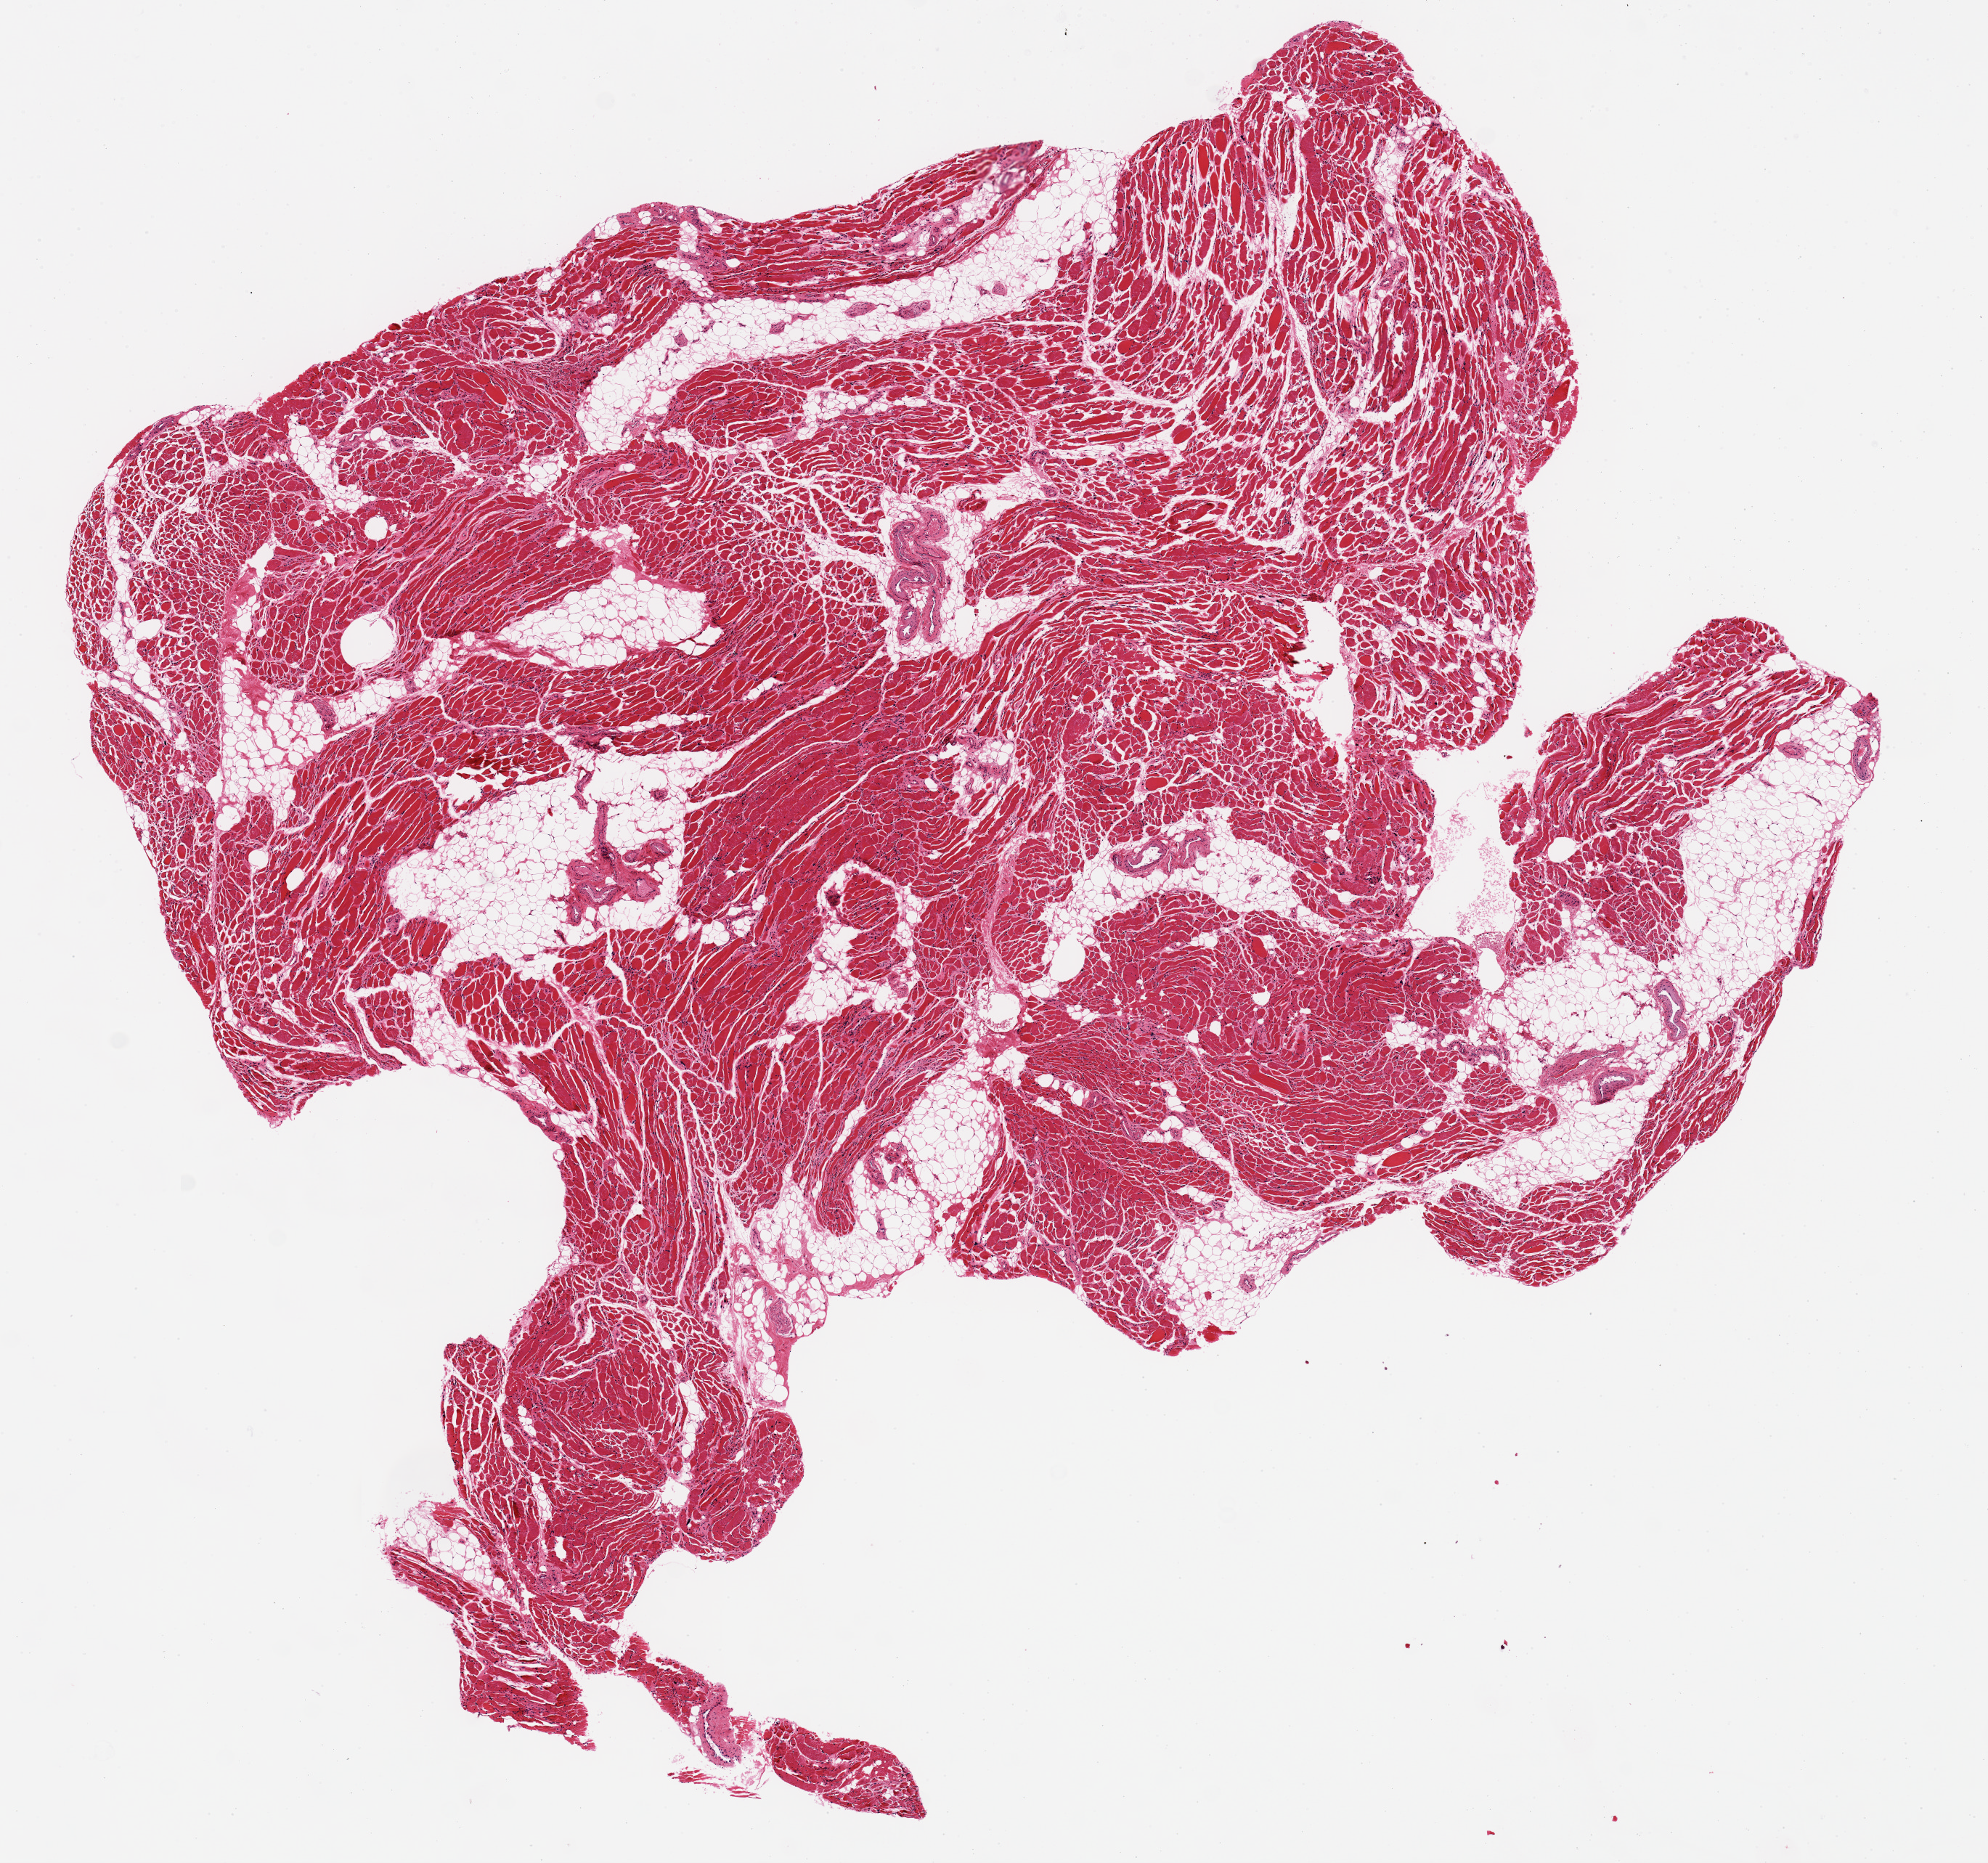
Whole-slide image, H&E stain, whole scanned area (about 10.8 x 10.1 mm) shown as a low-resolution overview; PAXgene-fixed paraffin-embedded (PFPE) section; section of skeletal muscle (target tissue); donor tissue sample. Female donor.
Reviewer comment on this tissue sample: ~20% intermingled adipose tissue.